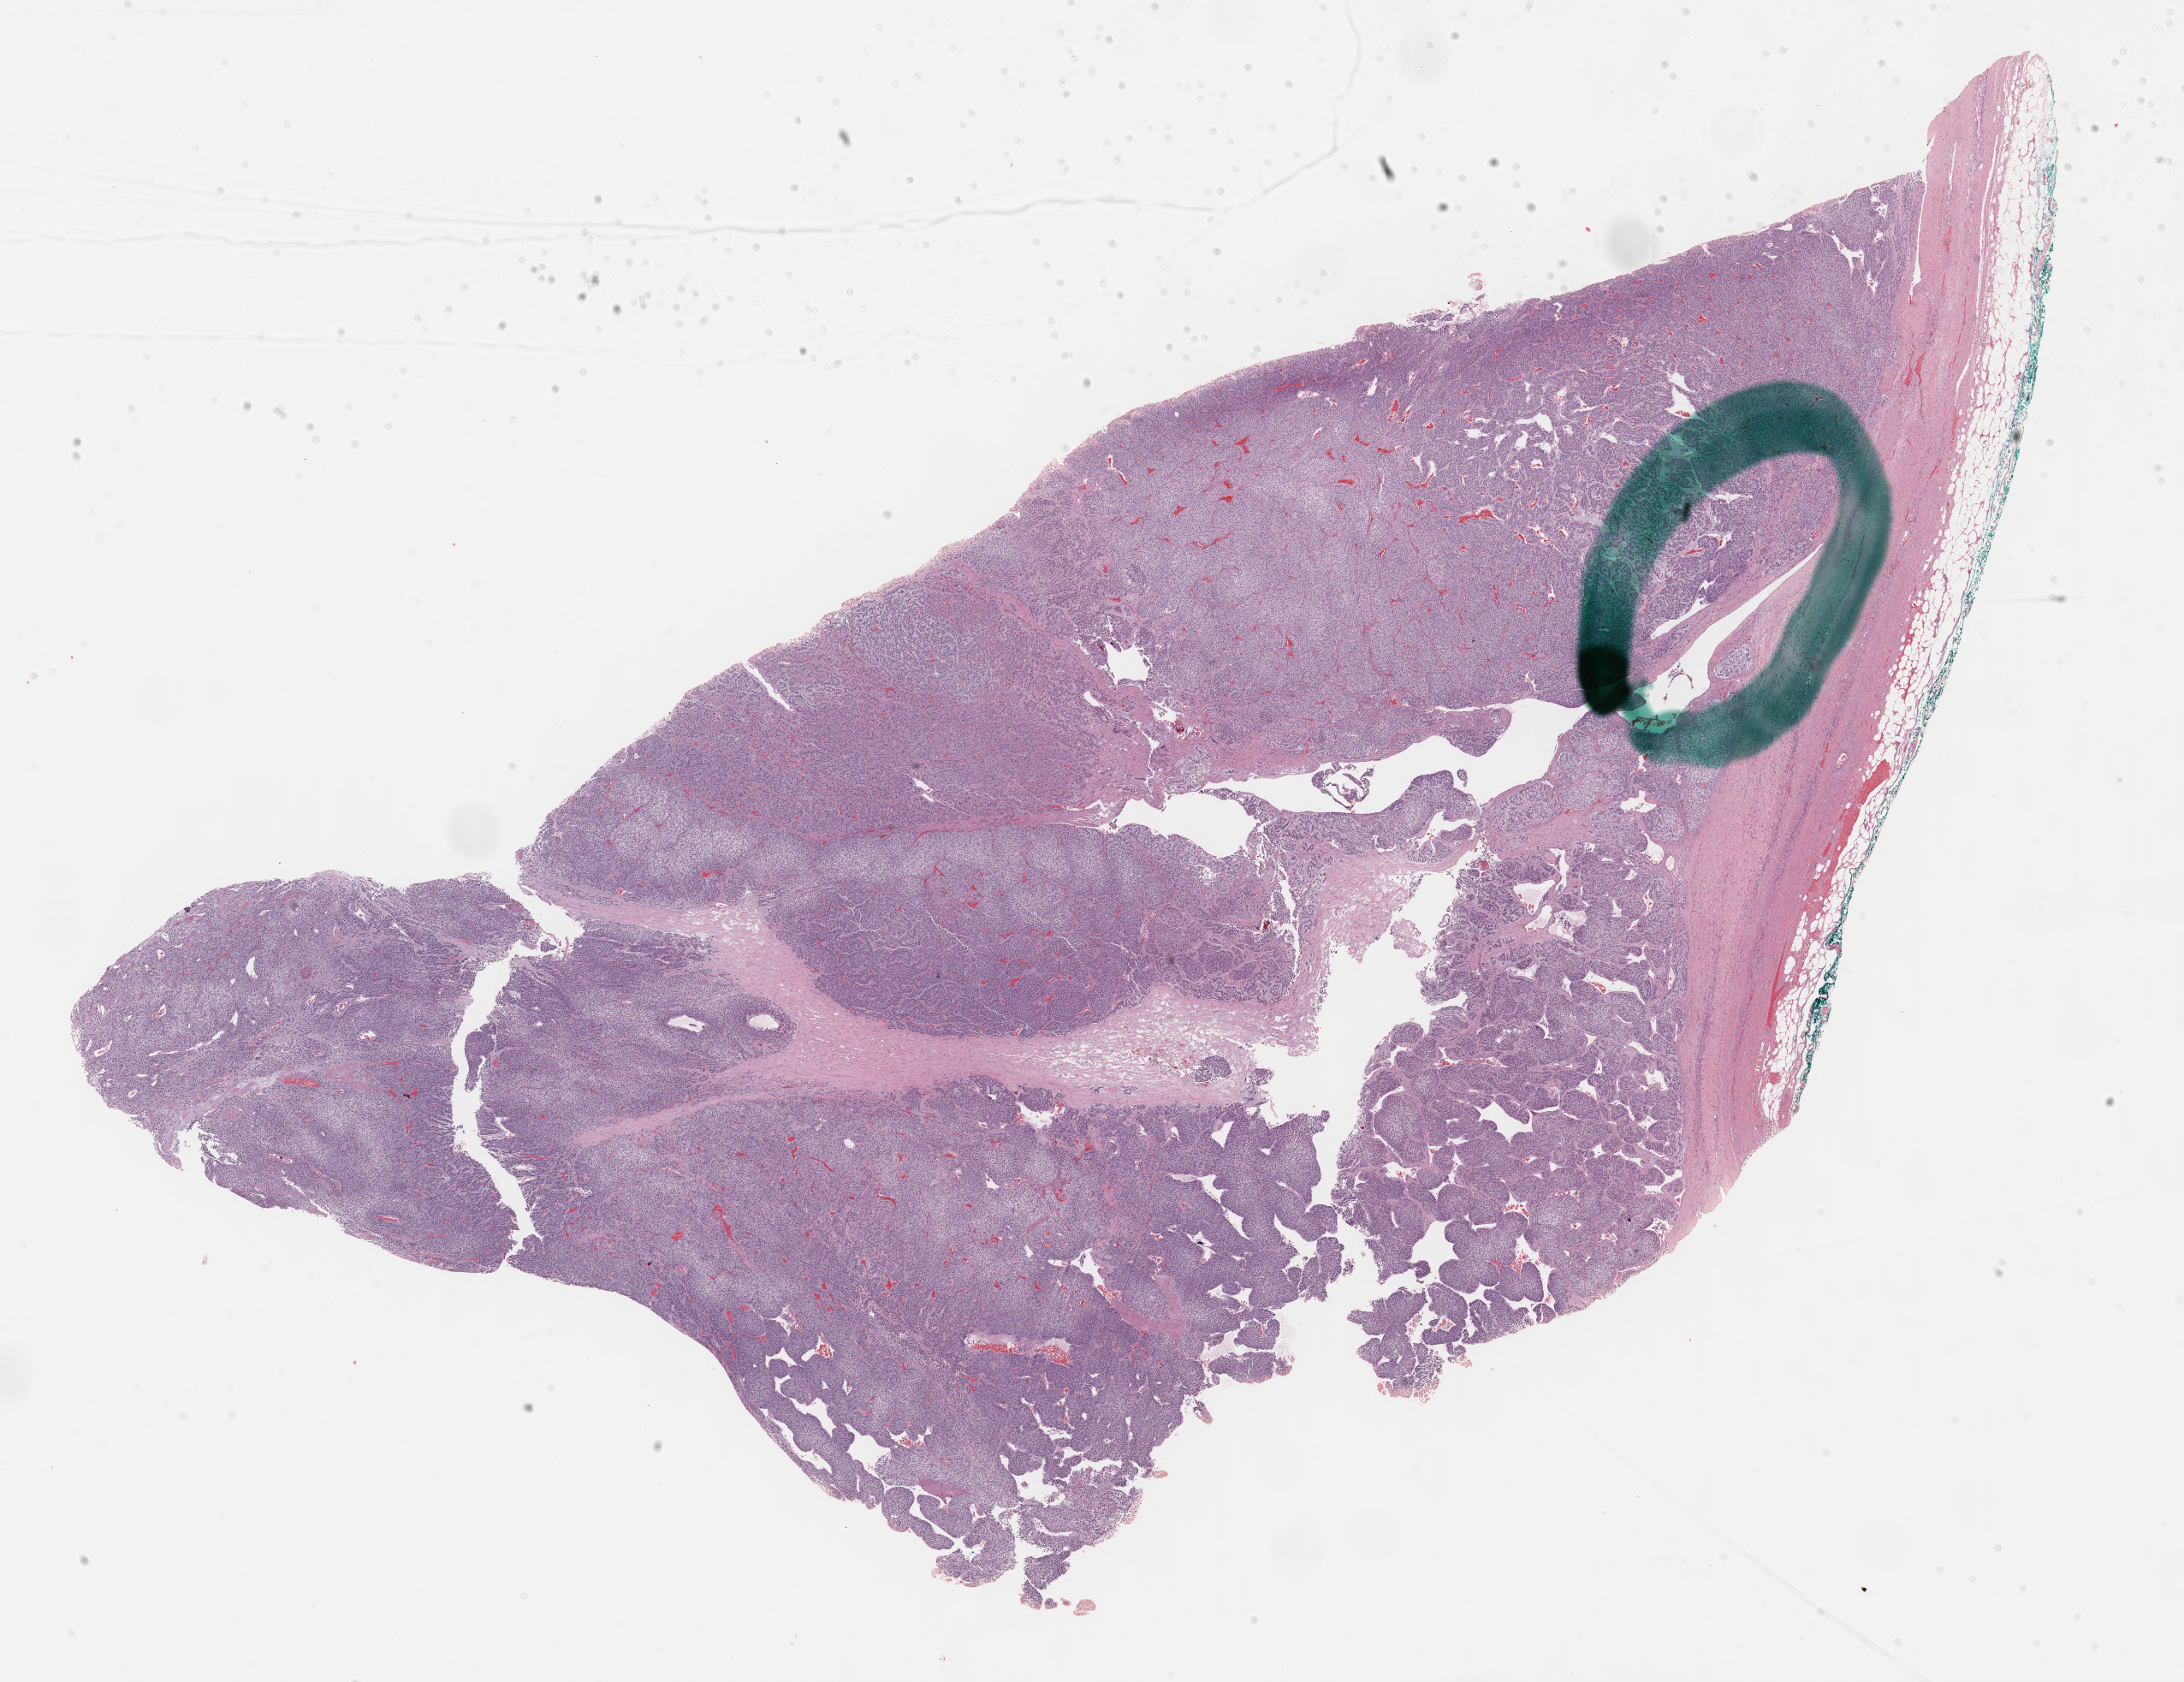
Digitized H&E tissue section (whole slide) — shown as a low-resolution overview of the whole scanned area (about 20.6 x 15.9 mm). FFPE section. Primary tumour sample from the adrenal cortex. Male, age 50 years at initial diagnosis.
* histologic diagnosis: Adrenal cortical carcinoma (cortex of adrenal gland)
* lymph nodes positive (case pathology): 0 of 1 examined